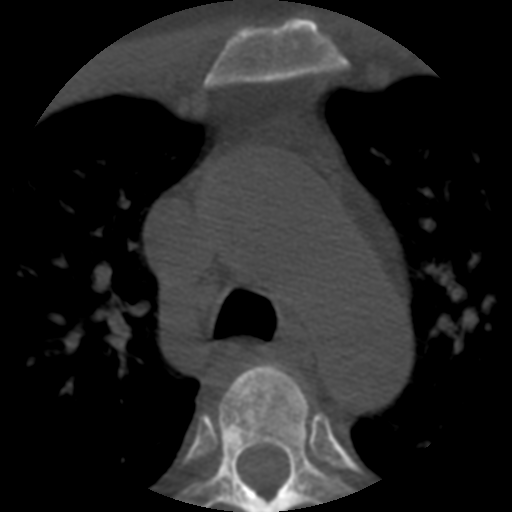
CT including the spine, one axial slice; position 398 of 508 along the scan axis; reconstruction kernel STANDARD; bone window (W 1800 / L 400 HU); 512 × 512 image matrix, field of view 160 × 160 mm. Patient age 57 years. From the clinical record (not read from this slice): primary cancer: prostate.
Annotated regions visible in this slice (semi-automatic segmentation, software-assisted and operator-edited):
- T3 vertebra: bounding box [x1, y1, x2, y2] px = [220, 362, 301, 412]
- T4 vertebra: [179, 377, 351, 512]